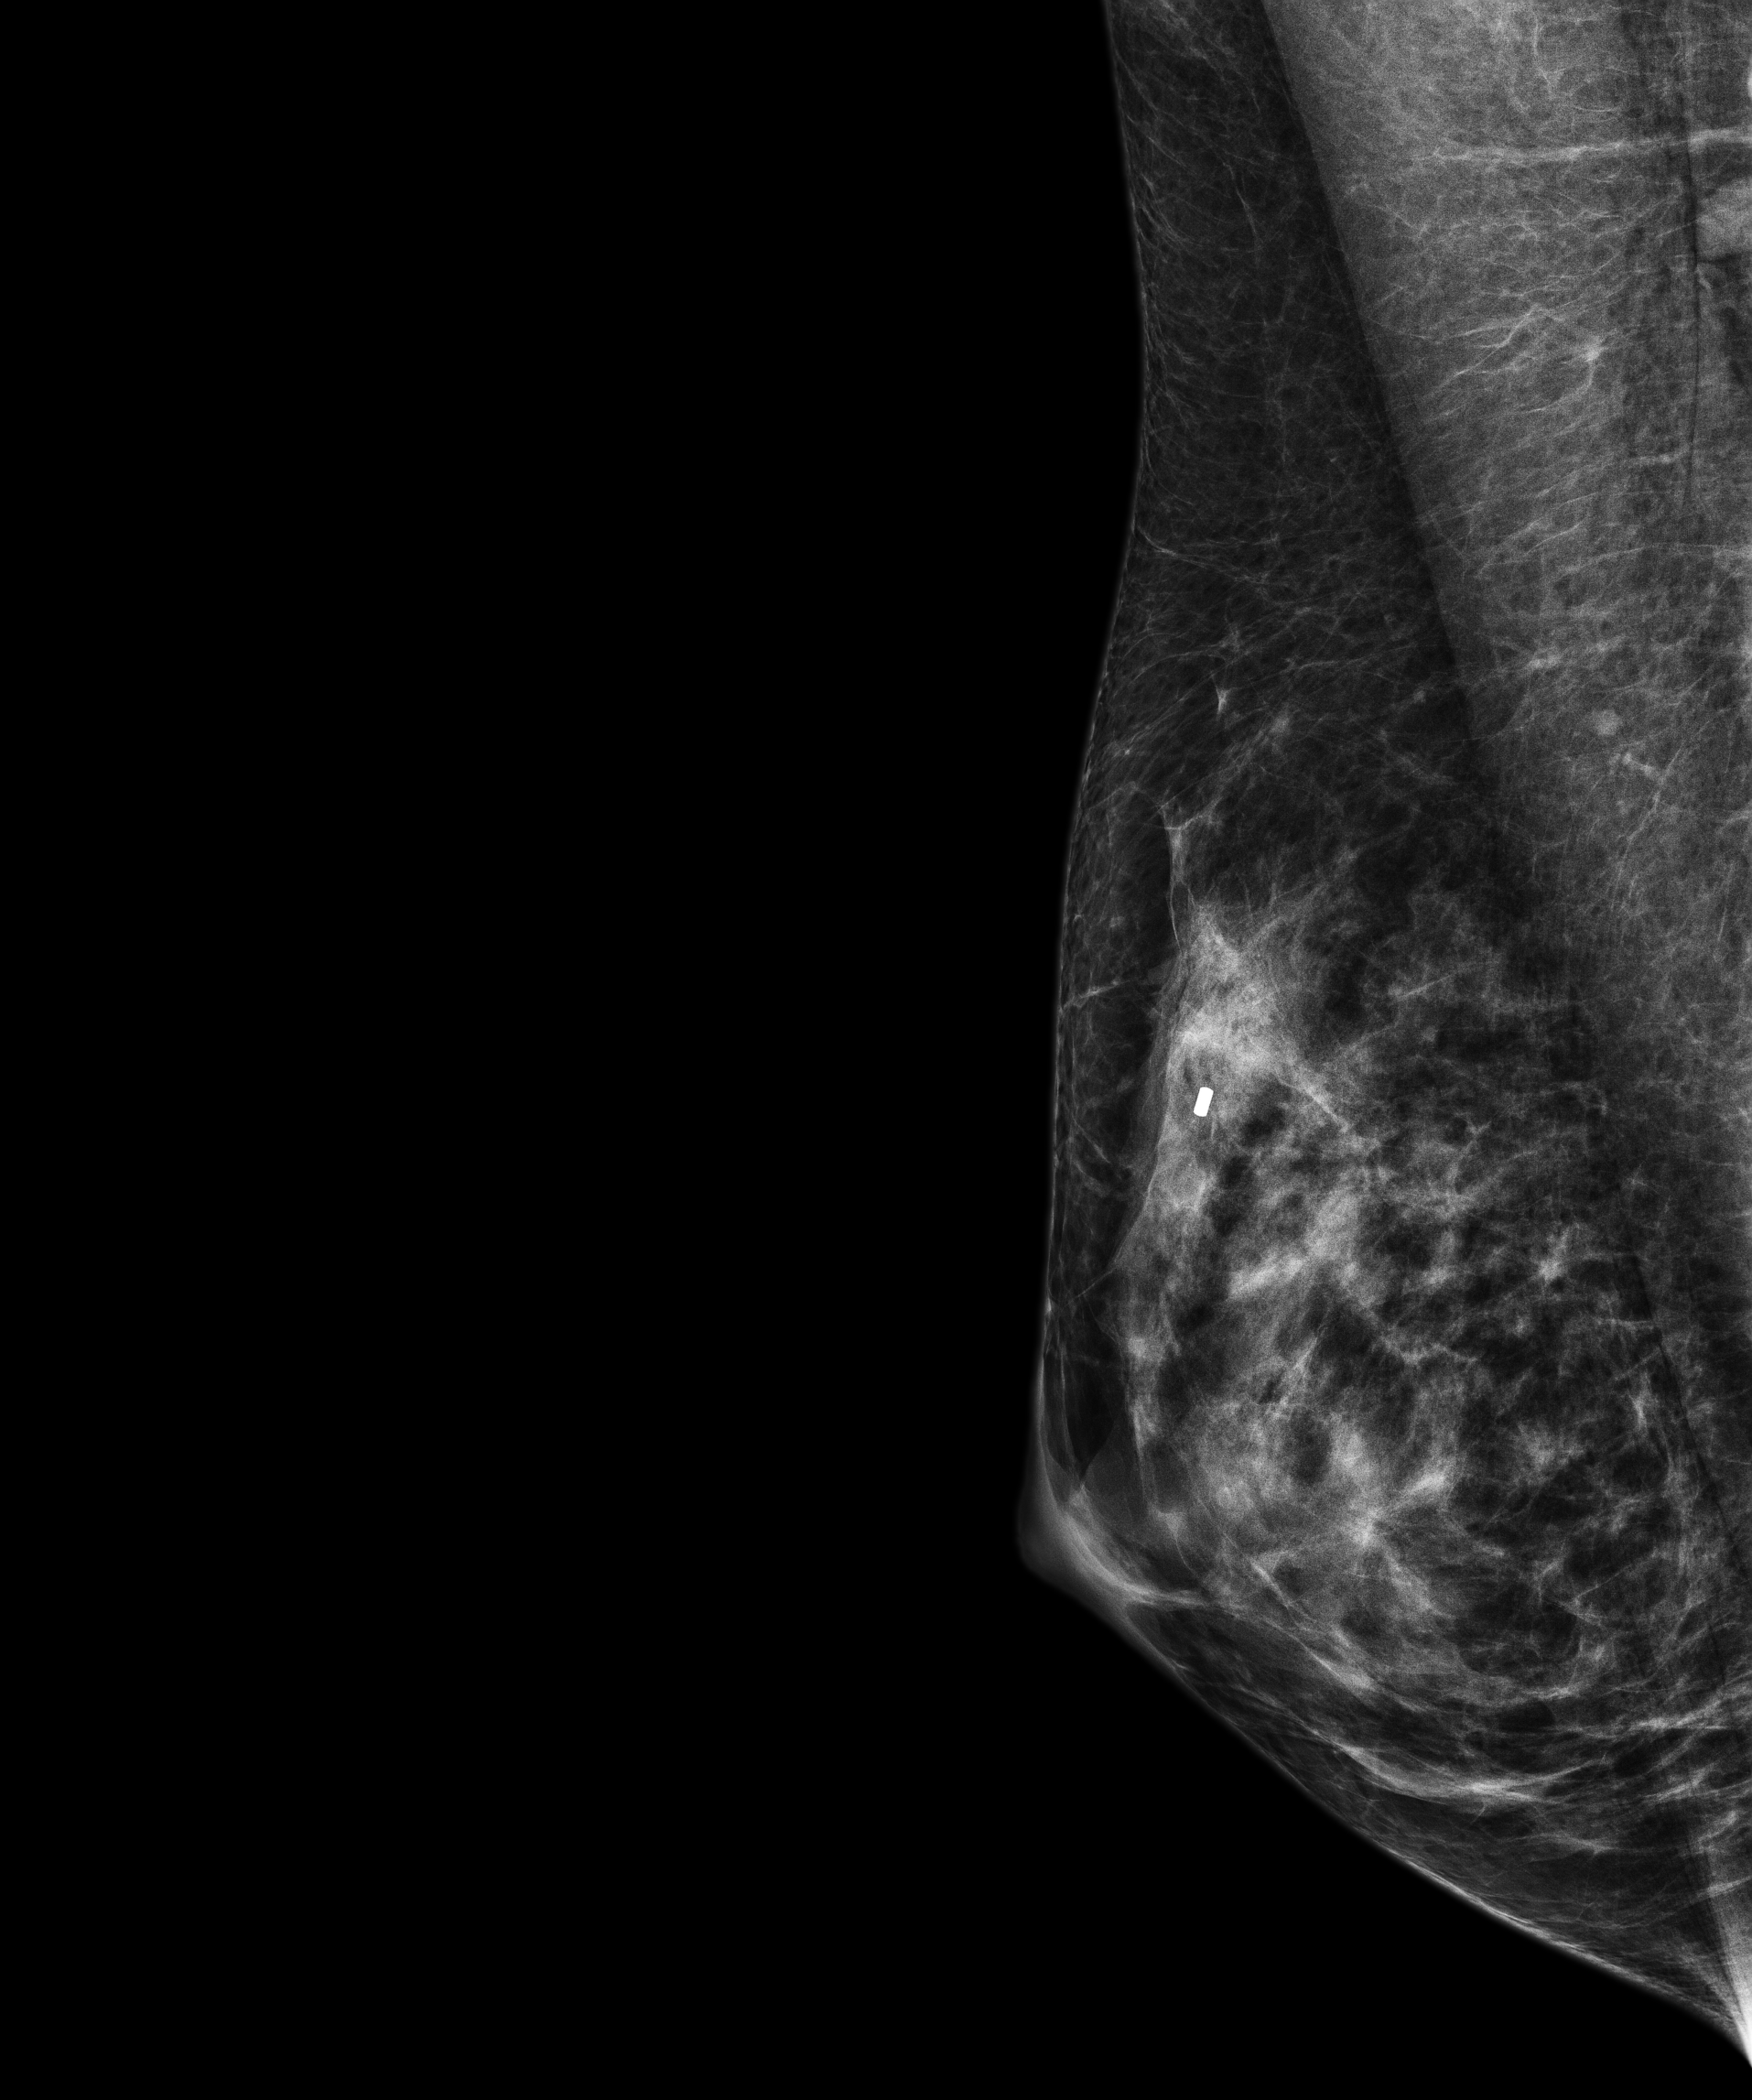
Annual screening mammography examination. Female patient, age 43 years.
Image type: full-field digital mammogram. Breast: right. Projection: MLO view.